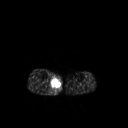
FDG PET of an extremity soft-tissue mass (from a PET/CT study), one axial slice. Position 128 of 267 along the scan axis. 3.27 mm slice thickness. 128 × 128 image matrix, field of view 500 × 500 mm. Patient: male, 69 years. Case-level facts recorded for this patient, not image findings: histological type: pleiomorphic liposarcoma; grade: high; site of the primary tumour: right calf.
Outlined on this slice (expert contour drawn on MRI and transferred to this co-registered scan by the dataset authors):
- gross tumour volume including surrounding oedema: bounding box (x1, y1, x2, y2) in pixels: (50, 76, 62, 94)
- gross tumour volume (mass): (51, 78, 62, 88)